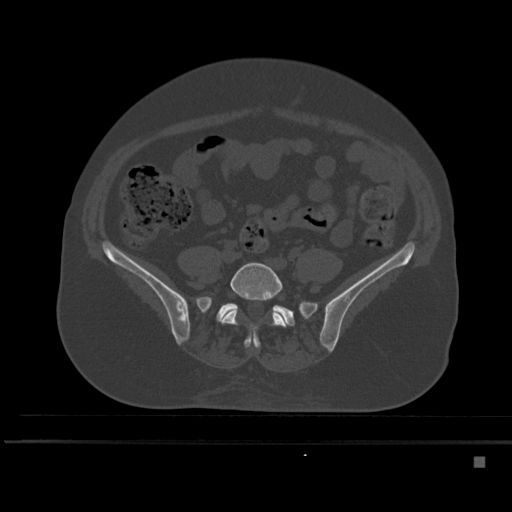
CT including the spine, one axial slice. Position 104 of 495 along the scan axis. Bone window (W 1800 / L 400 HU). 1.5 mm slice thickness. 512 × 512 image matrix, field of view 404 × 404 mm. Patient: female, 33 years. From the clinical record (not read from this slice): primary cancer: breast.
Structures marked on this image (semi-automatic segmentation, software-assisted and operator-edited):
- L5 vertebra: box from (x=220, y=262) to (x=287, y=349) px